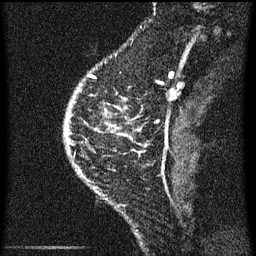
Breast MRI (dynamic contrast-enhanced), one sagittal slice. Slice 18 of 60 in the series (ordered by position). Dynamic contrast-enhanced series, image 2 of 3 at this slice position (ordered by acquisition). 1.5 T. TE 4.2 ms, TR 8 ms. 256 × 256 image matrix. Female patient, age 46 years.
Annotated regions visible in this slice (semi-automatically segmented with operator editing):
- analysis volume of interest (the breast-tissue region the enhancement analysis was run in; not a lesion): bounding box (x1, y1, x2, y2) in pixels: (95, 68, 145, 195)
- tumour enhancement mask (voxels above the 70 % enhancement threshold inside the analysis volume of interest): (95, 100, 140, 153)